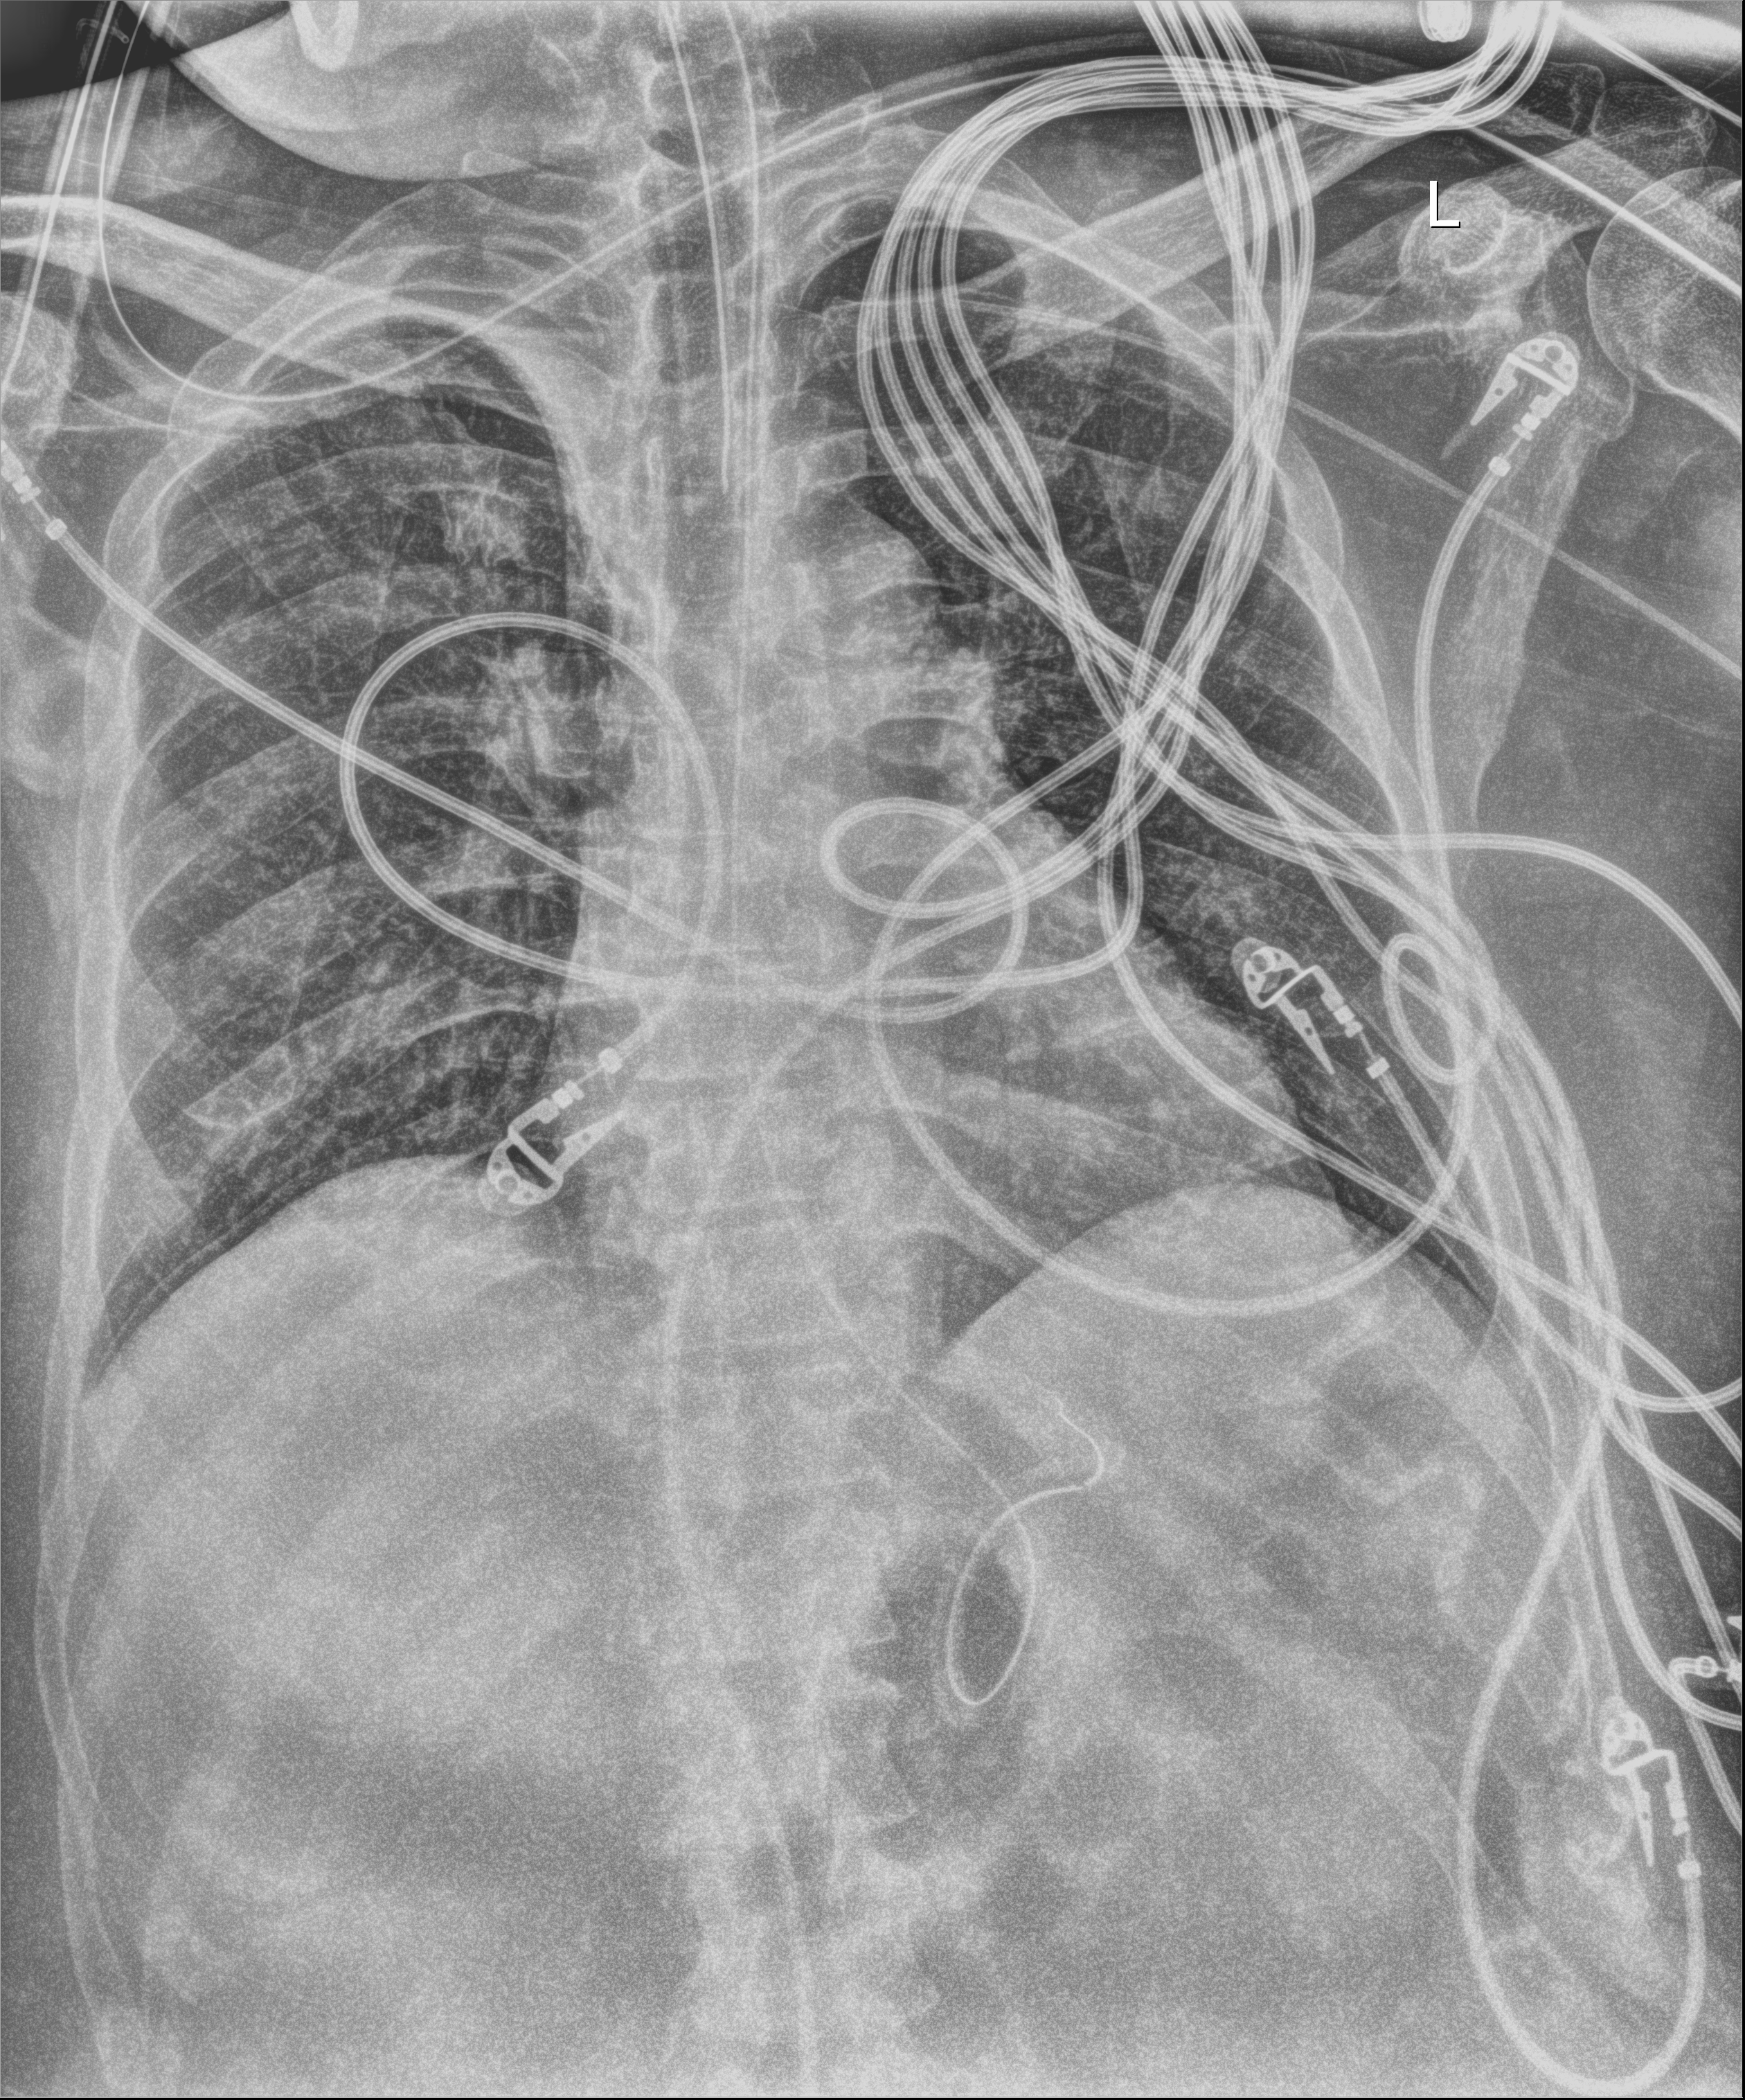
Chest X-ray (portable). Adult patient hospitalised with COVID-19, age 18–59 years.
Admission-level facts for this patient (not findings on this image; timing relative to this image not recorded): admitted to intensive care during this hospital stay: yes; mechanically ventilated during this hospital stay: yes; hypertension (admission record): no.